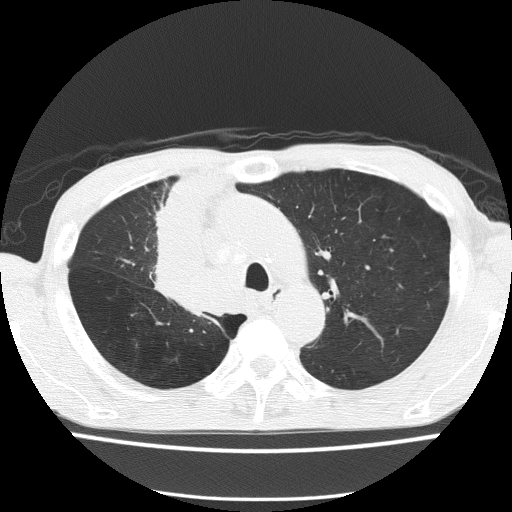
Low-dose screening chest CT, one axial slice. Slice 107 of 150 in the series (ordered by position). Reconstruction kernel FC51. 120 kVp. Lung window (W 1500 / L -600 HU). 2 mm slice thickness. 512 × 512 image matrix, field of view 336 × 336 mm.
Structures marked on this image (outlined manually by an expert reader):
- lesion 1 (tumor, hilum of right lung): bounding box [x1, y1, x2, y2] px = [157, 184, 242, 312]